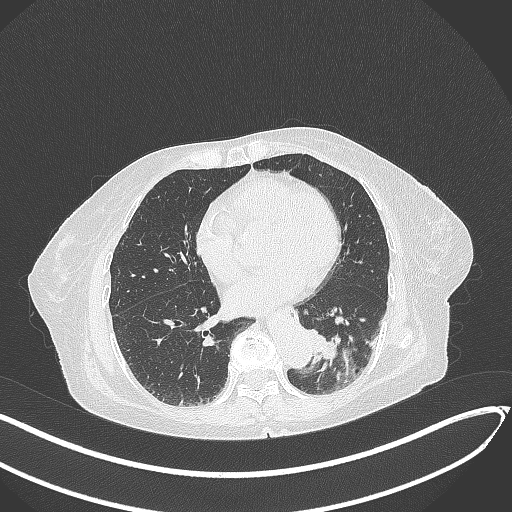
Chest CT, one axial slice. Slice 92 of 324 in the series (ordered by position). Reconstruction kernel B70f. Lung window (W 1500 / L -600 HU). 1 mm slice thickness. 512 × 512 image matrix, field of view 400 × 400 mm. Patient: female, 82 years. Case-level facts recorded for this patient, not image findings: clinical TNM (as recorded): T1b N0 M1.
Outlined on this slice (bounding box drawn by a radiologist):
- lung tumour (recorded histology: adenocarcinoma): bounding box [x1, y1, x2, y2] px = [303, 323, 345, 373]